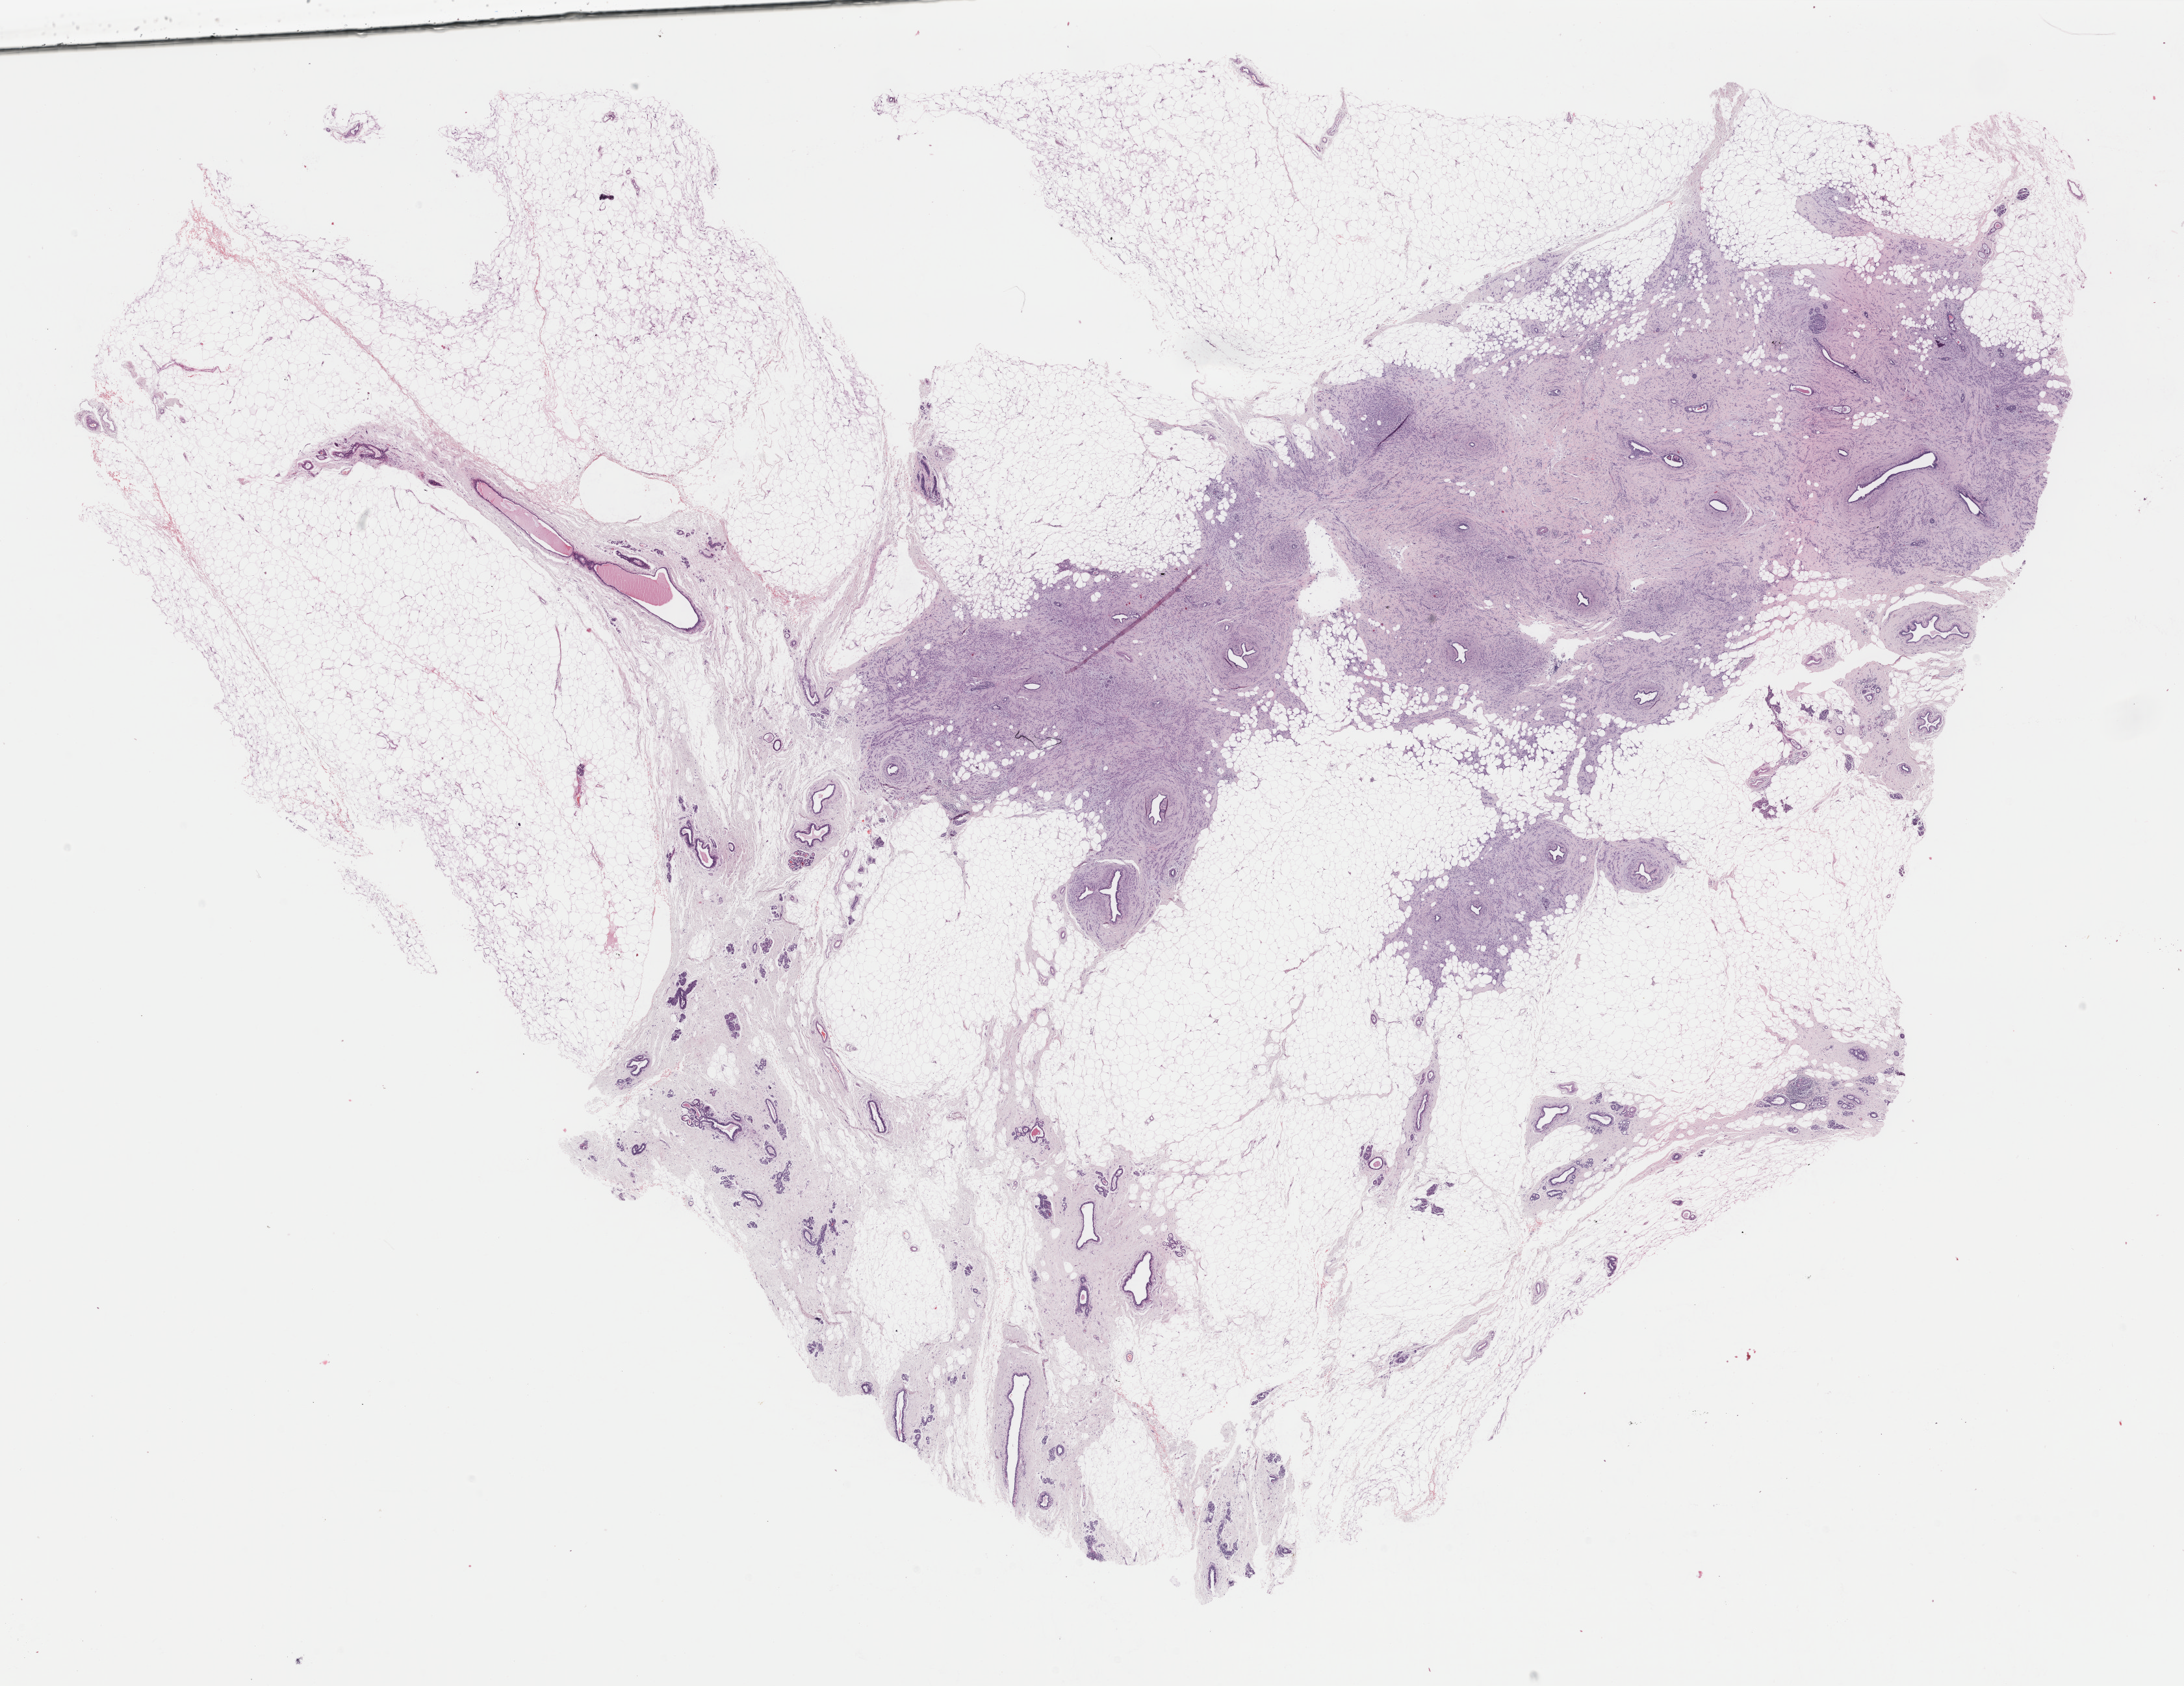
Whole-slide histology image, H&E — whole scanned area (about 26.7 x 20.6 mm) shown as a low-resolution overview; formalin-fixed paraffin-embedded (FFPE) diagnostic section; primary tumour sample from the breast. Female, age 68 years at initial diagnosis.
AJCC pathologic stage: IA (7th edition). Histologic diagnosis: Lobular carcinoma, NOS. TNM: T1c N0 M0. Lymph nodes positive (case pathology): 0 of 1 examined. Laterality: right.